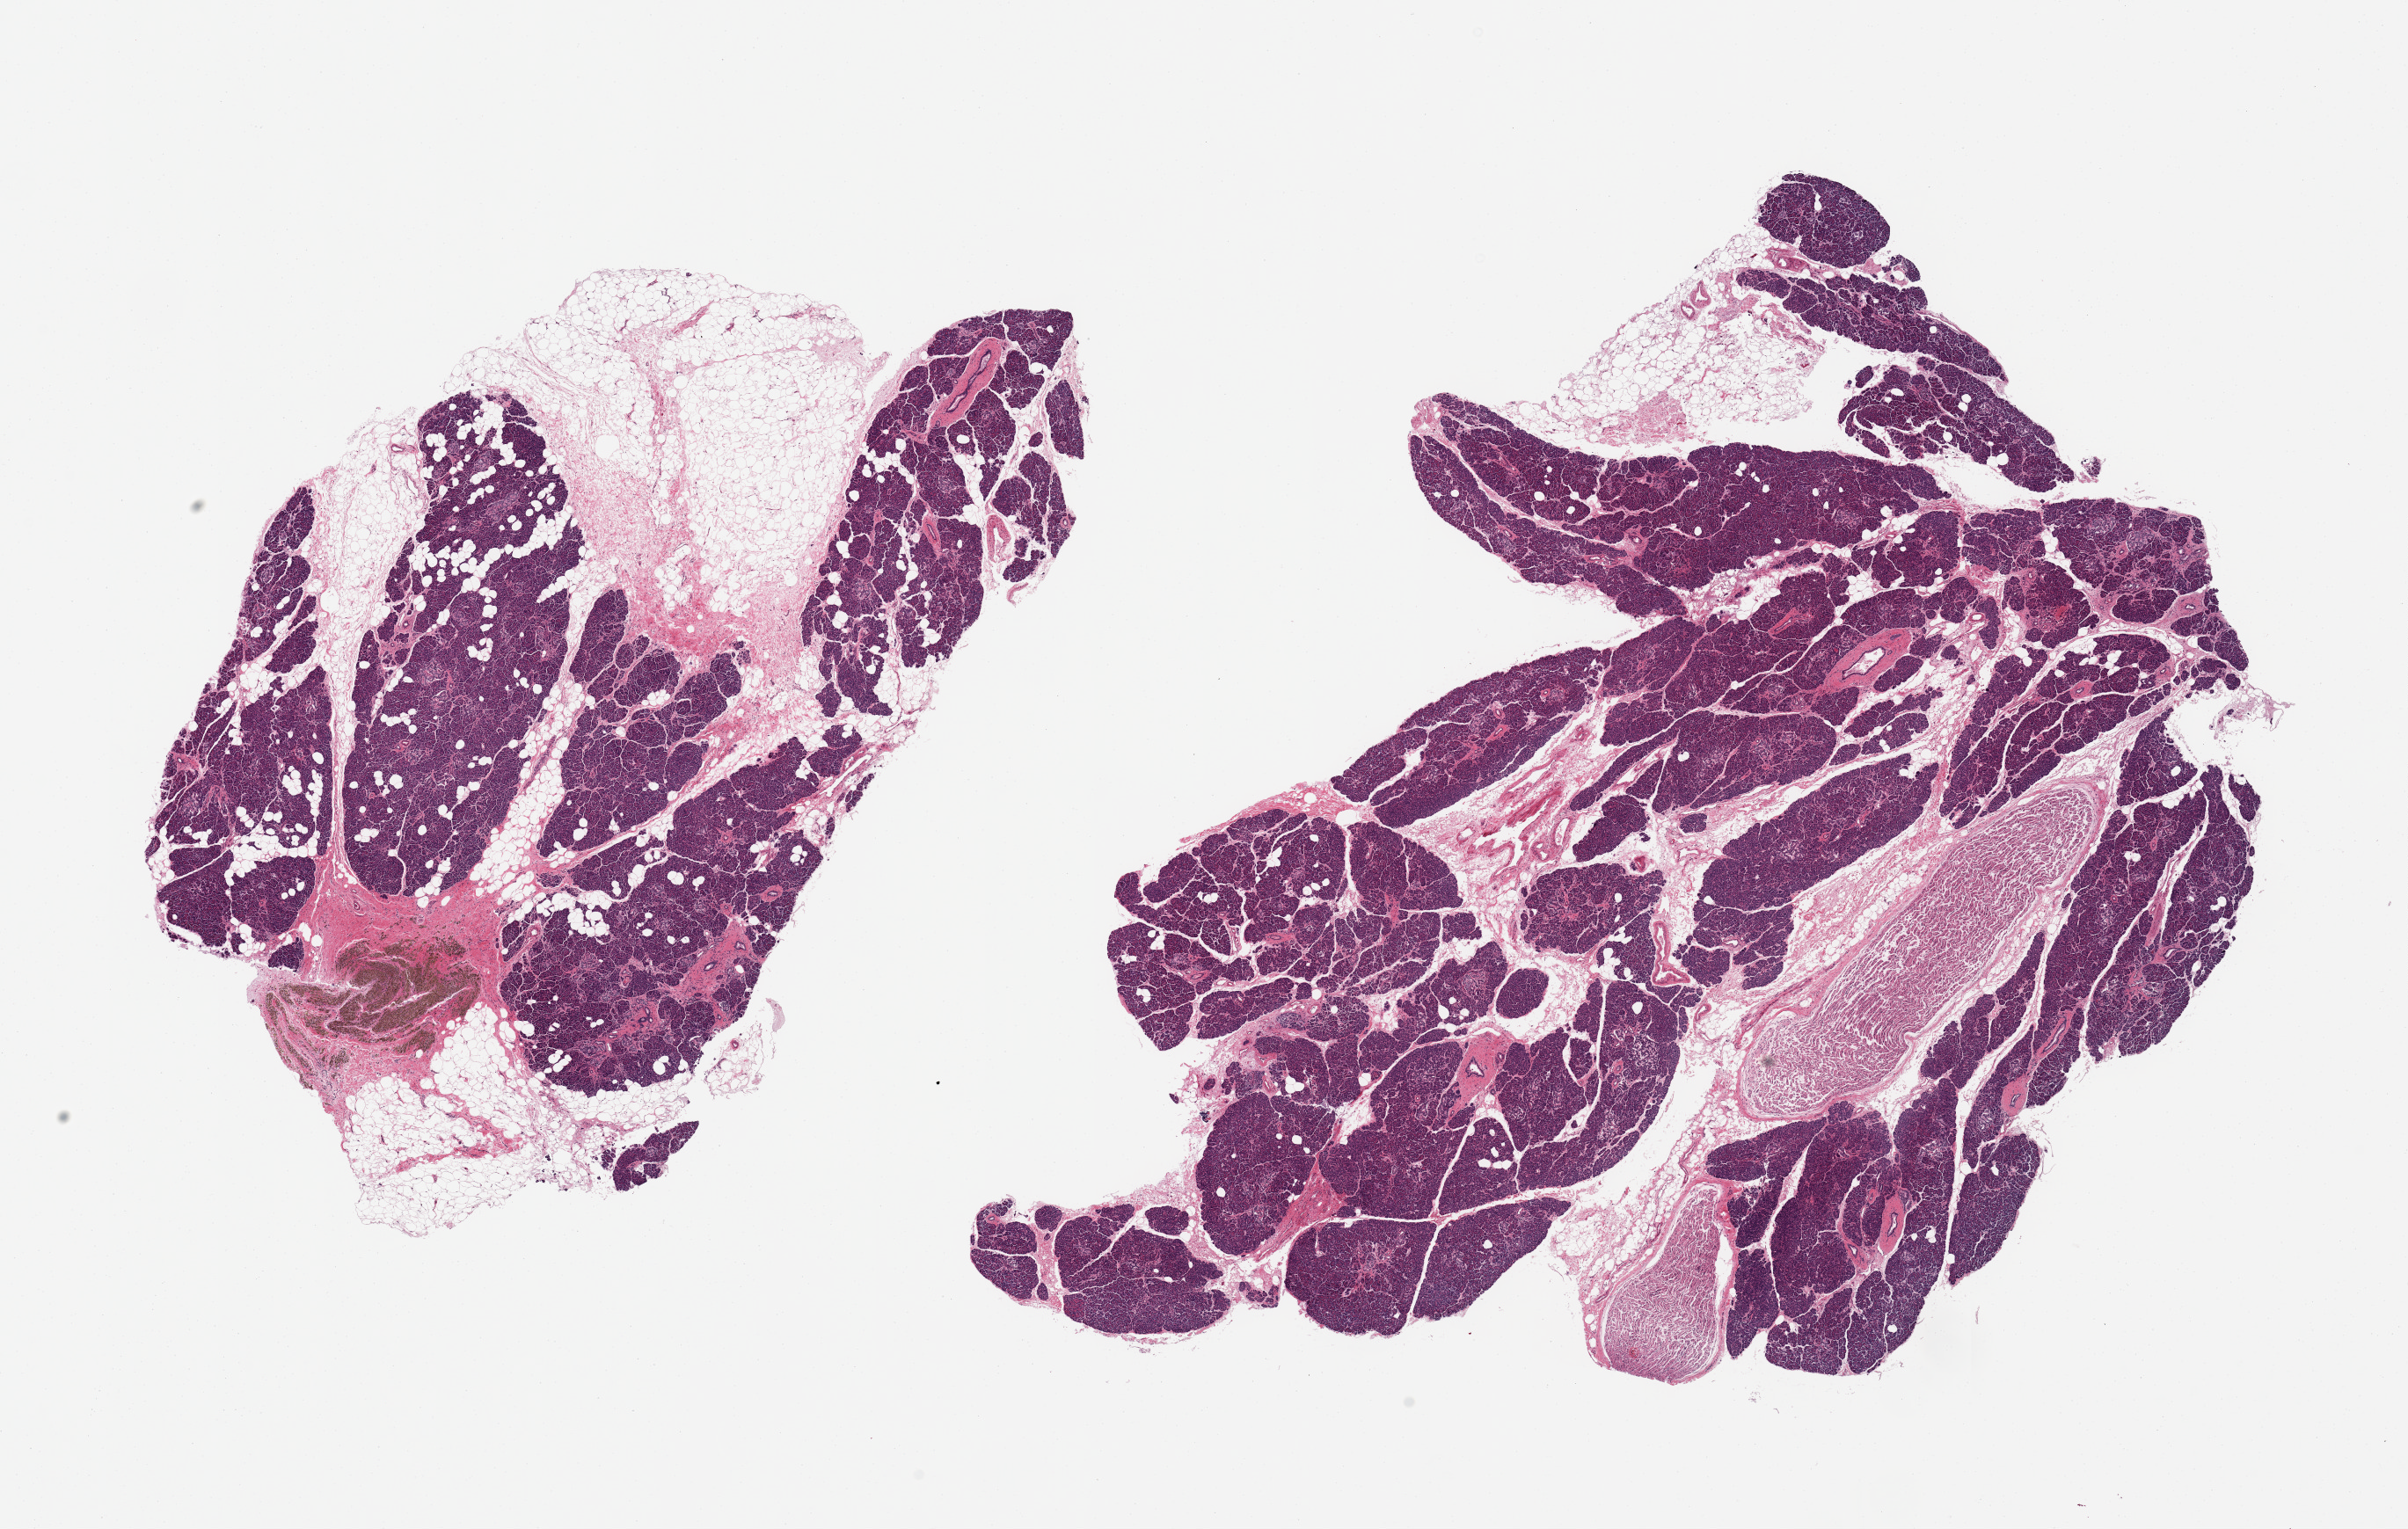
Digitized hematoxylin and eosin (H&E)-stained section, shown as a low-resolution overview of the whole scanned area (about 21.7 x 13.8 mm, acquisition: 20x scan); PAXgene-fixed paraffin-embedded (PFPE) section; target tissue: pancreas; tissue donor sample. Donor: female.
Pathologist's review note for this sample: 2 pieces: 50% fat in 1 piece; other piece has large internal nerve (10%); focus of pigmented macrophages 1x1.5 mm.